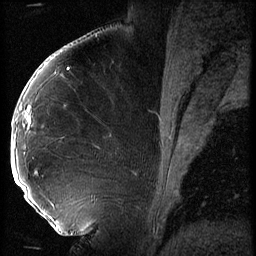
Breast MRI (dynamic contrast-enhanced), one sagittal slice; slice 29 of 56 in the series (ordered by position); 3 images stored at this slice position (order not interpretable as contrast timing); 1.5 T; TE 4.2 ms, TR 9 ms; 256 × 256 image matrix, field of view 180 × 180 mm. Patient: female, 43 years. Case-level facts recorded for this patient, not image findings: setting: breast cancer imaged before/during neoadjuvant chemotherapy; receptor status: HER2-positive.
Annotated regions visible in this slice (semi-automatically segmented with operator editing):
- analysis volume of interest (the breast-tissue region the enhancement analysis was run in; not a lesion): box from (x=12, y=92) to (x=74, y=211) px
- tumour enhancement mask (voxels above the 140 % enhancement threshold inside the analysis volume of interest): (x=12, y=107)–(x=30, y=189)